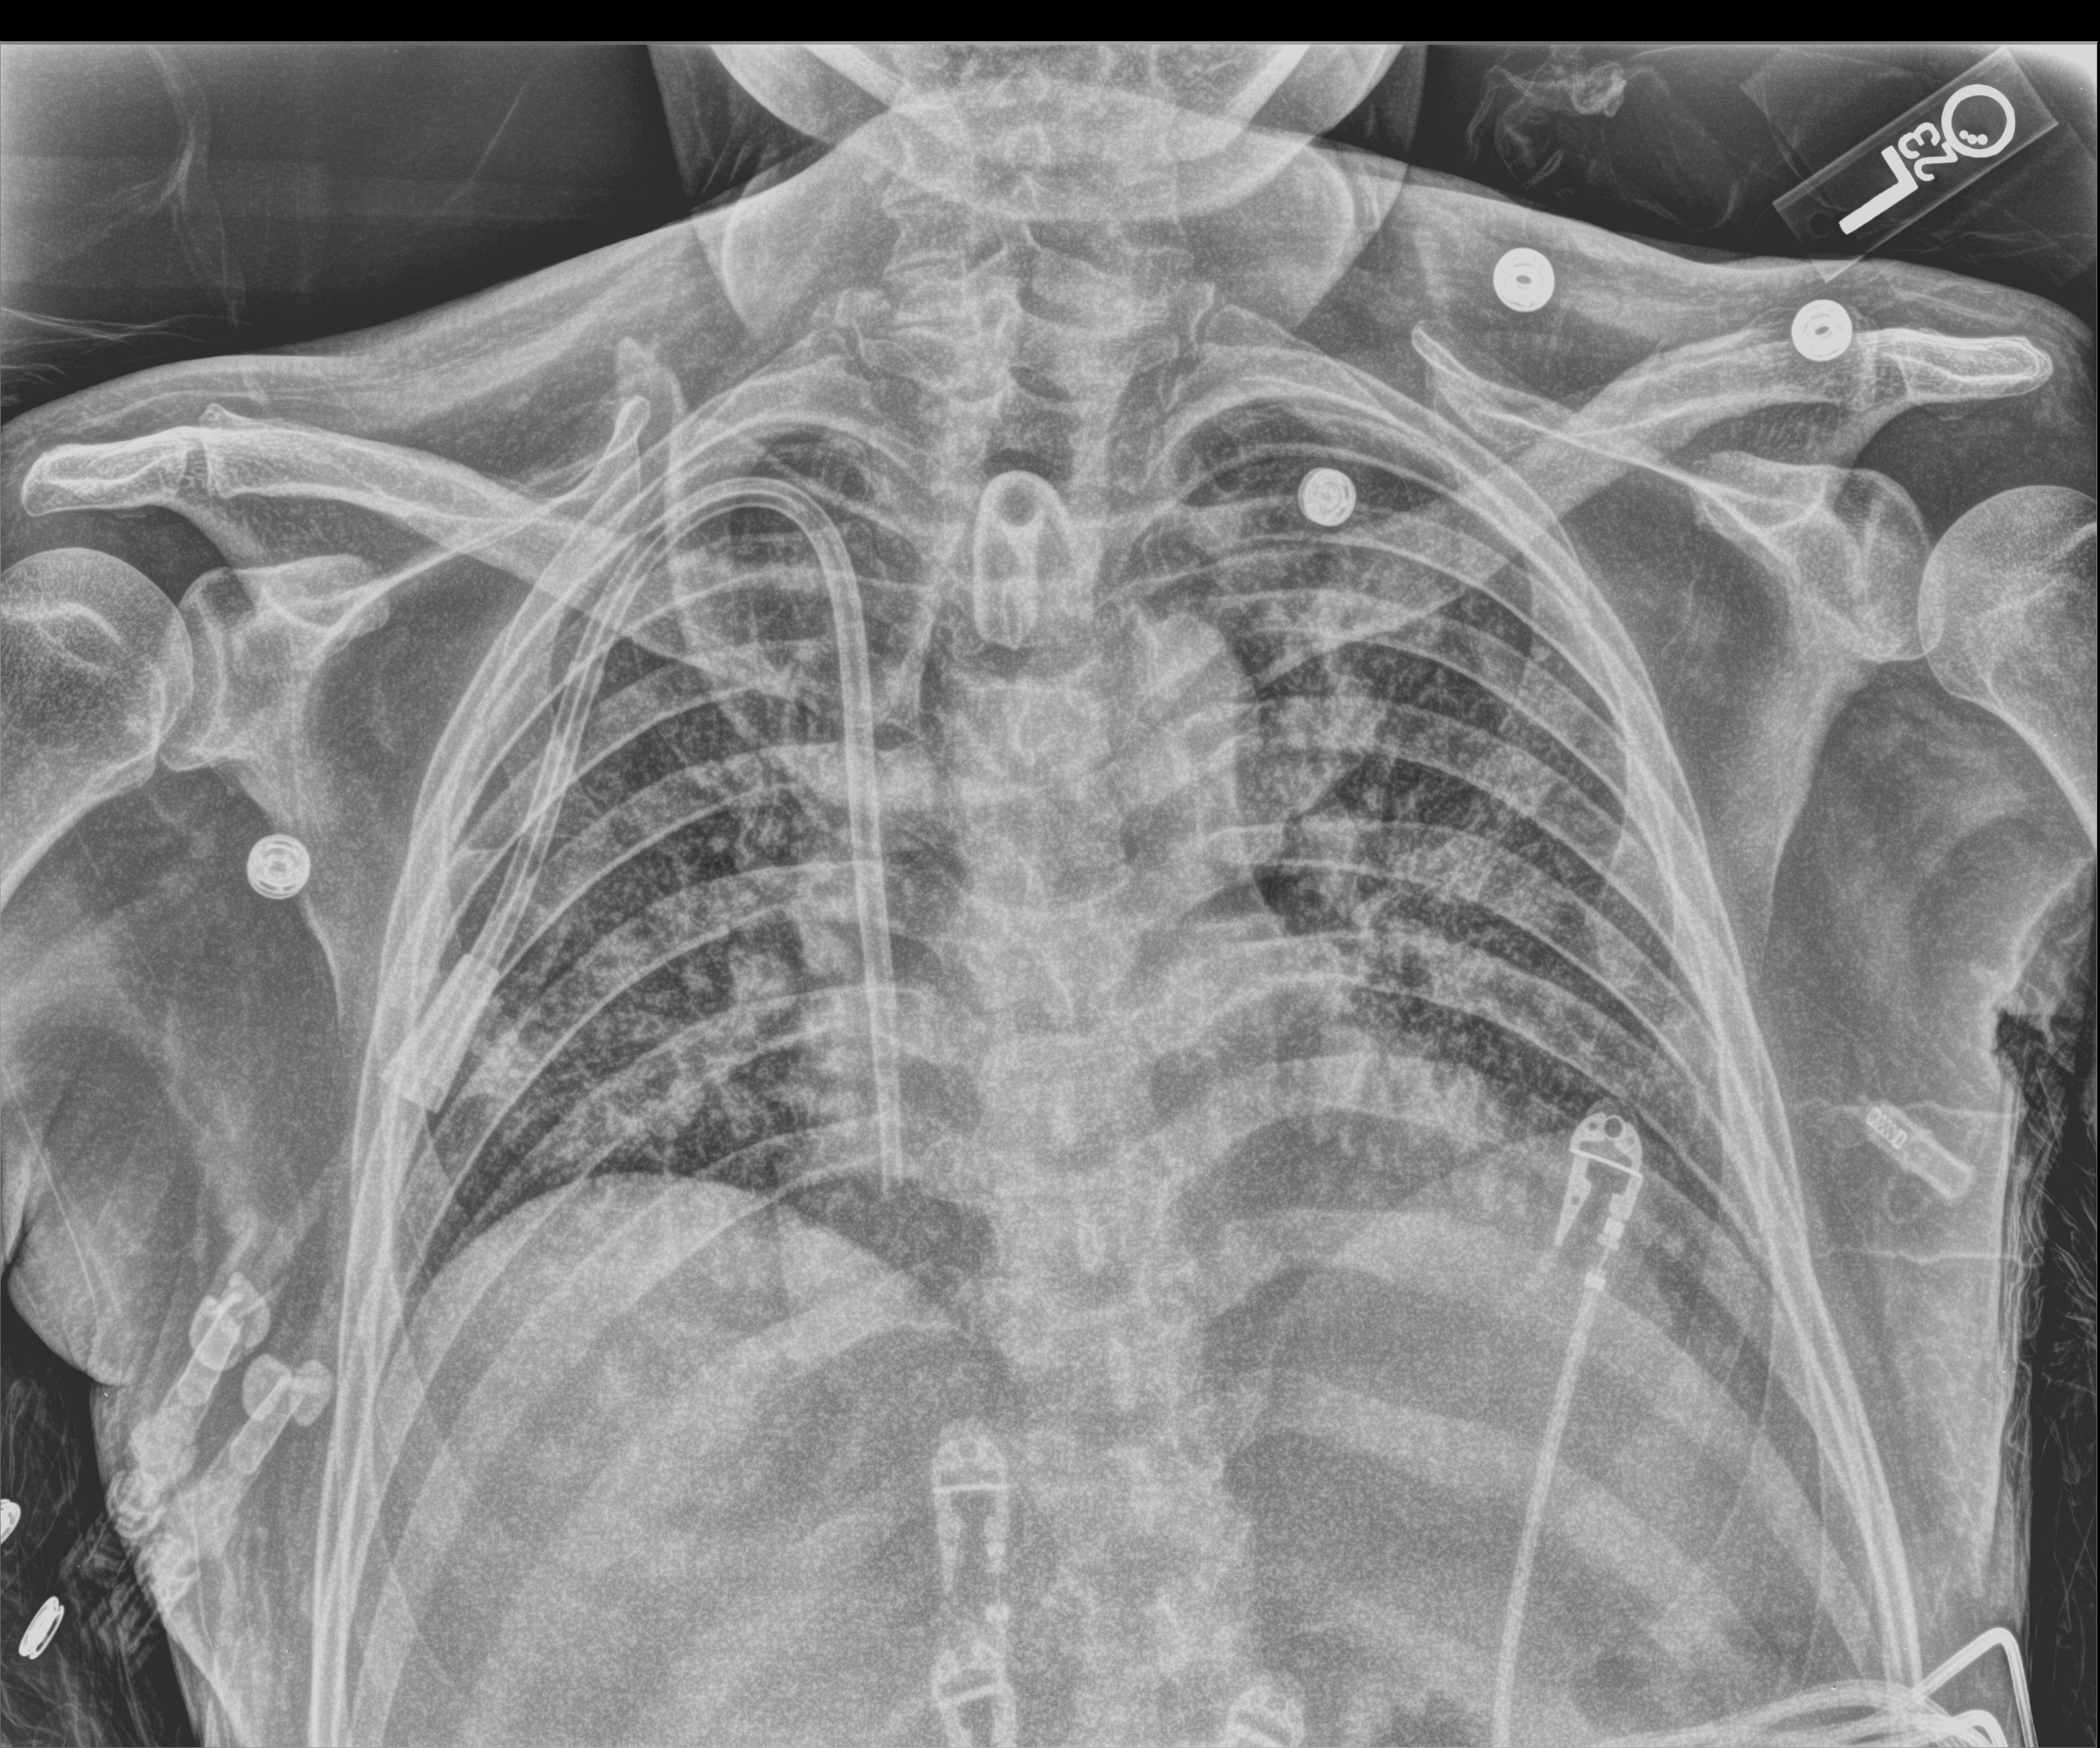
Bedside chest radiograph (computed radiography), anteroposterior (AP) projection. Male patient hospitalised with COVID-19, age 18–59 years.
From the hospital-stay record, not from the radiograph (when in the stay this image was taken is not recorded): admitted to intensive care during this hospital stay: yes; COPD (admission record): no.